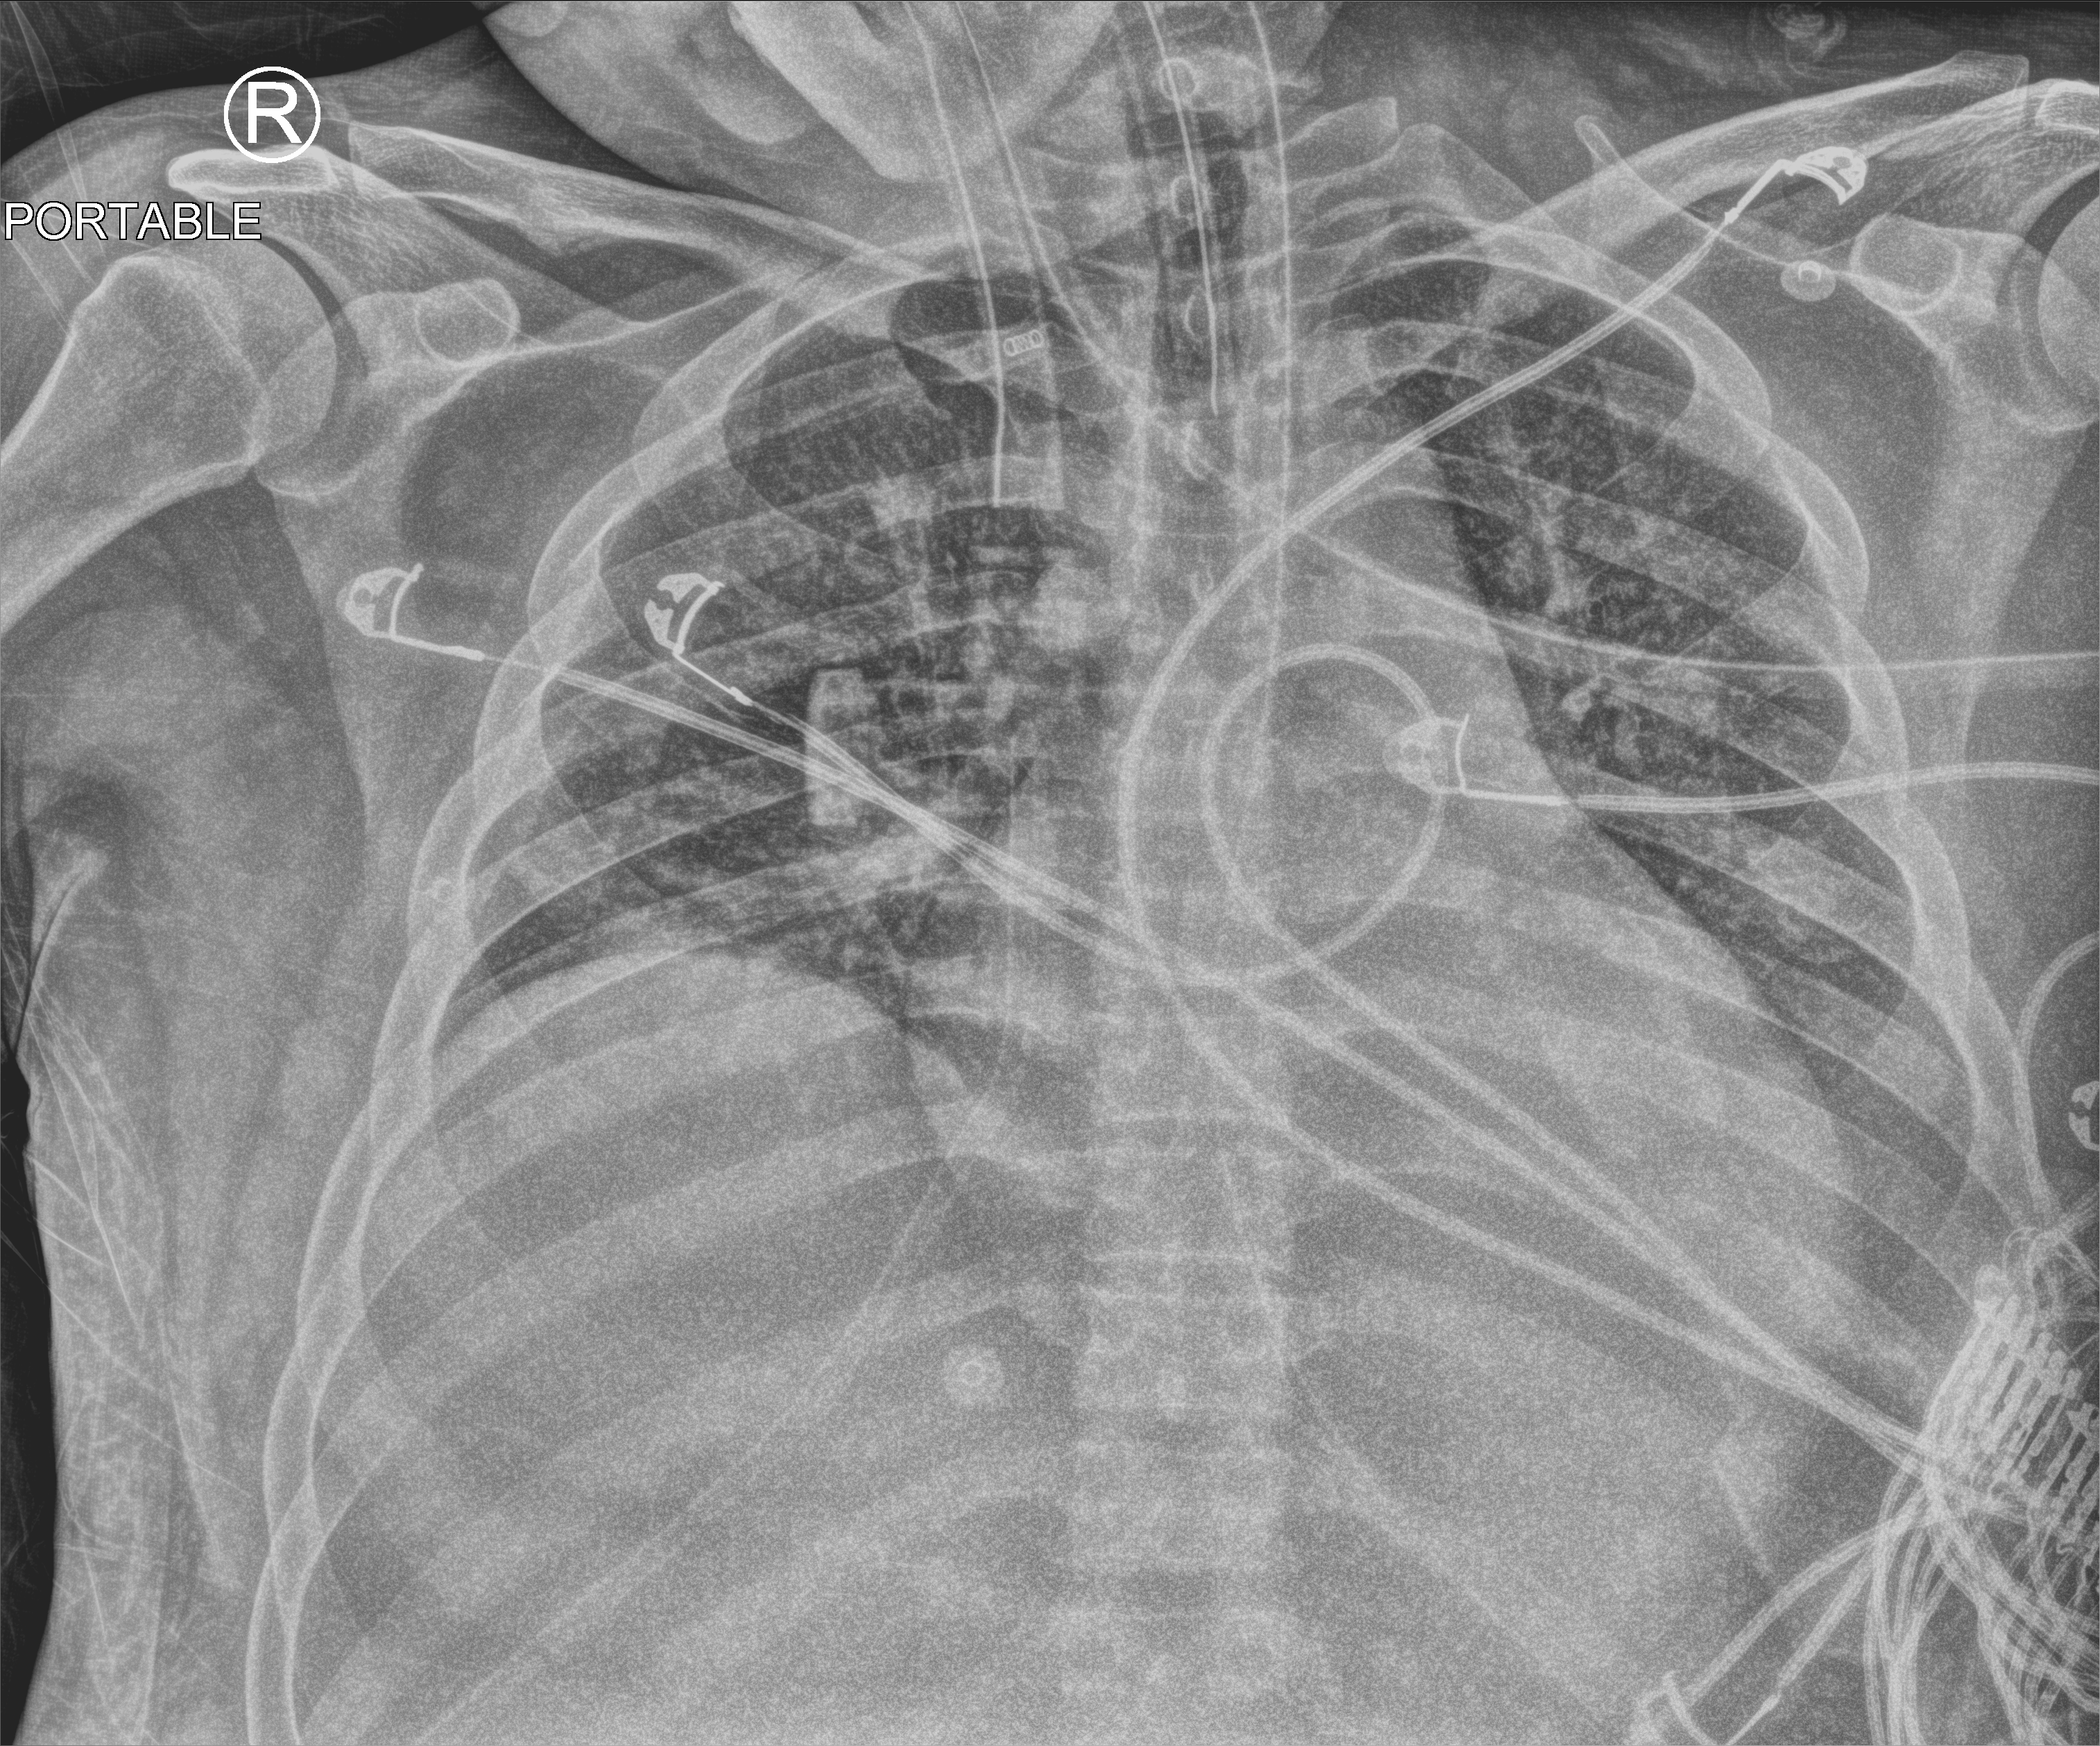
Portable chest radiograph. Male patient hospitalised with COVID-19, age 18–59 years.
Hospital-stay facts (about this admission, not read from this image; timing relative to this image not recorded): length of hospital stay: 61 days; mechanically ventilated during this hospital stay: yes.